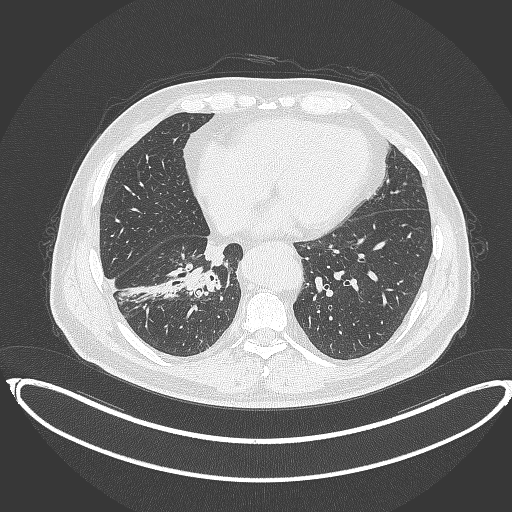
Chest CT, one axial slice. Reconstruction kernel B70f. Lung window (W 1500 / L -600 HU). 512 × 512 image matrix. Patient: male, 61 years. Case-level facts recorded for this patient, not image findings: clinical TNM (as recorded): T1b N1 M0.
Structures marked on this image (bounding box drawn by a radiologist):
- lung tumour (recorded histology: squamous cell carcinoma): bounding box [x1, y1, x2, y2] px = [182, 260, 222, 302]